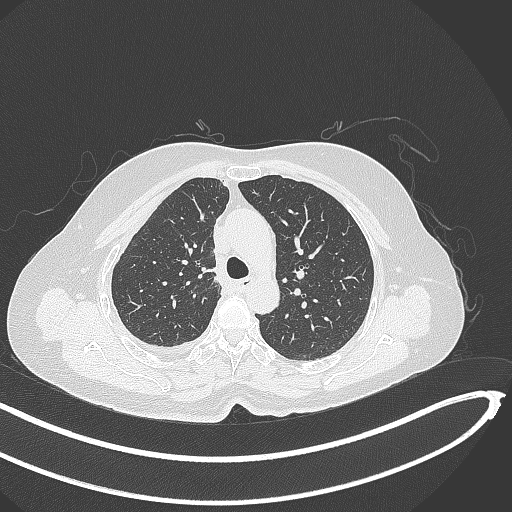
Chest CT, one axial slice. Position 266 of 345 along the scan axis. Lung window (W 1500 / L -600 HU). 1 mm slice thickness. 512 × 512 image matrix, field of view 400 × 400 mm. Female patient, age 64 years. From the clinical record (not read from this slice): clinical TNM (as recorded): T1b N0 M1.
Outlined on this slice (bounding box drawn by a radiologist):
- lung tumour (recorded histology: adenocarcinoma): box from (x=194, y=260) to (x=218, y=286) px